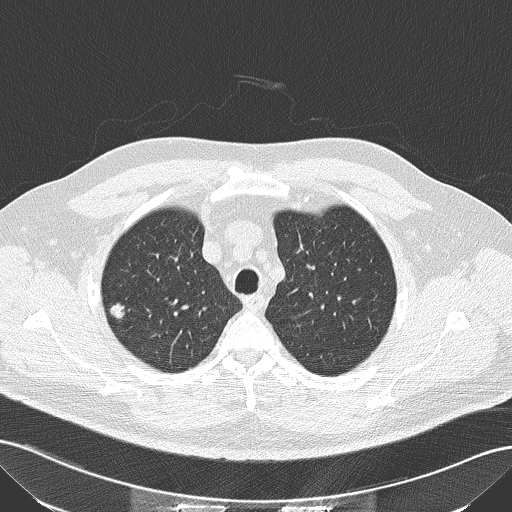
Low-dose screening chest CT, axial slice. Second annual screen. Lung window (W 1500 / L -600 HU). Lung (sharp) reconstruction kernel (B50f). 512 × 512 image matrix, field of view 360 × 360 mm. Male, age 56 years at enrolment. Current smoker at enrolment.
Lesion marked by an expert reader, bounding box <96,292,143,331> (left, top, right, bottom; pixels). The exam's reader record, not a measurement of the box and not confirmed to be the same lesion: non-calcified nodule or mass ≥4 mm, right upper lobe, 10 × 9 mm, spiculated (stellate) margins, soft tissue attenuation, pre-existing on the prior screen: no. Lung cancer was diagnosed 117 days after this screen: squamous cell carcinoma, NOS, right upper lobe, moderately differentiated (G2), stage IA (AJCC 6th edition), 10 mm at pathology.